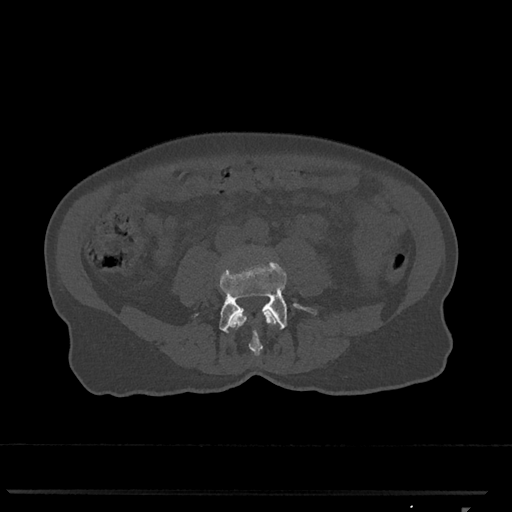
CT including the spine, one axial slice. Slice 230 of 793 in the series (ordered by position). Reconstruction kernel Br40s/3. 120 kVp. Bone window (W 1800 / L 400 HU). 512 × 512 image matrix, field of view 380 × 380 mm. Patient: female, 62 years. From the clinical record (not read from this slice): primary cancer: renal.
Outlined on this slice (semi-automatic segmentation, software-assisted and operator-edited):
- L3 vertebra: bounding box [x1, y1, x2, y2] px = [230, 310, 276, 356]
- L4 vertebra: [195, 261, 316, 333]